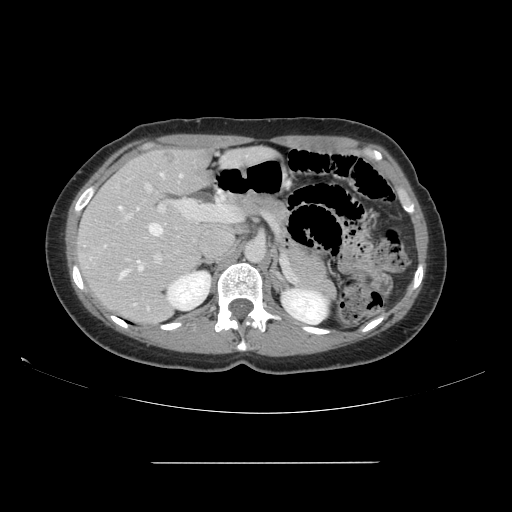
Contrast-enhanced abdominal CT, one axial slice. Slice 96 of 151 in the series (ordered by position). Intravenous contrast given. Soft-tissue window (W 400 / L 40 HU). 2.5 mm slice thickness. 512 × 512 image matrix, field of view 421 × 421 mm. Female patient, age 46 years. Case-level facts recorded for this patient, not image findings: diagnosis: colorectal cancer liver metastases, imaged before liver resection; multiple liver metastases: yes; largest metastasis: 3 cm; disease in both lobes: yes.
Annotated regions visible in this slice (manually delineated by an expert):
- hepatic veins: bounding box <105,173,183,278> (left, top, right, bottom; pixels)
- liver: <78,149,211,323>
- planned liver remnant (the part of the liver to remain after resection): <90,151,211,260>
- portal vein (with intrahepatic branches): <123,182,236,264>
- liver metastasis: <164,152,179,164>